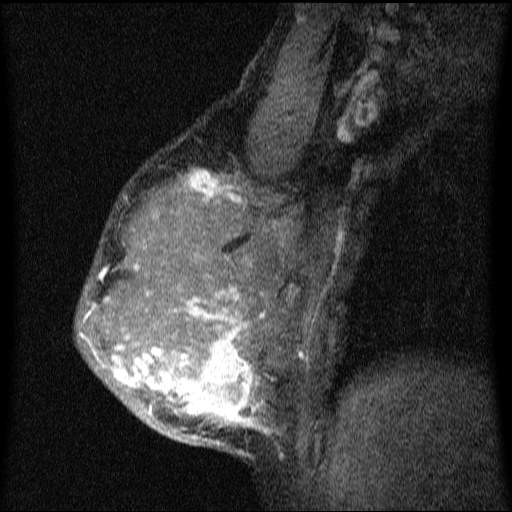
Breast MRI (dynamic contrast-enhanced), one sagittal slice; slice 45 of 64 in the series (ordered by position); dynamic contrast-enhanced series, image 2 of 4 at this slice position (ordered by acquisition); 1.5 T; TE 4.2 ms, TR 9.1 ms; 512 × 512 image matrix, field of view 180 × 180 mm. Patient: female, 33 years.
Structures marked on this image (semi-automatic segmentation, software-assisted and operator-edited):
- analysis volume of interest (the breast-tissue region the enhancement analysis was run in; not a lesion): box from (x=76, y=151) to (x=336, y=457) px
- tumour enhancement mask (voxels above the 70 % enhancement threshold inside the analysis volume of interest): (x=81, y=169)–(x=305, y=446)